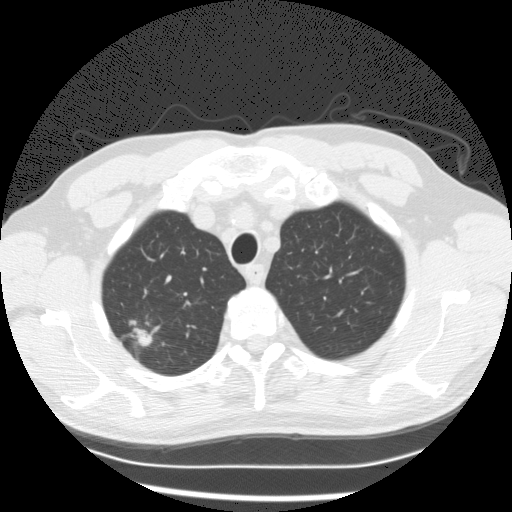
Chest CT (low-dose screening protocol), one axial image. First (baseline) screen. Lung window (W 1500 / L -600 HU). 2.5 mm slice thickness. Slice 23 of 132 in the series. Male participant, aged 63 years at enrolment.
Lesion marked by an expert reader, bounding box [x1, y1, x2, y2] px = [104, 304, 170, 364]. Screening reader's record for this exam (one nodule recorded; not confirmed to be the boxed lesion): non-calcified nodule or mass ≥4 mm, right upper lobe, 19 × 9 mm, poorly defined margins, mixed attenuation.